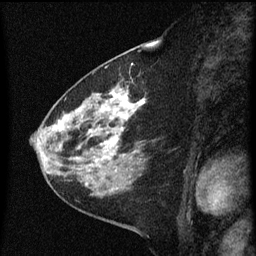
Breast MRI (dynamic contrast-enhanced), one sagittal slice; slice 25 of 60 in the series (ordered by position); dynamic contrast-enhanced series, image 2 of 3 at this slice position (ordered by acquisition); 1.5 T; TE 4.2 ms, TR 8 ms; 256 × 256 image matrix, field of view 180 × 180 mm. Female patient, age 60 years.
Annotated regions visible in this slice (semi-automatic segmentation, software-assisted and operator-edited):
- analysis volume of interest (the breast-tissue region the enhancement analysis was run in; not a lesion): box from (x=48, y=82) to (x=156, y=183) px
- tumour enhancement mask (voxels above the 70 % enhancement threshold inside the analysis volume of interest): (x=59, y=92)–(x=142, y=163)